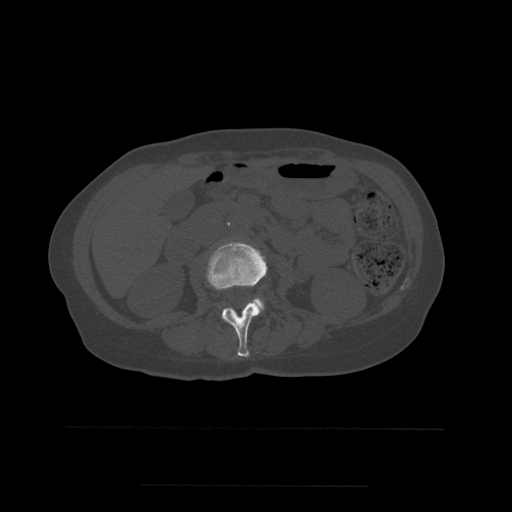
CT including the spine, one axial slice. Slice 204 of 544 in the series (ordered by position). Bone window (W 1800 / L 400 HU). 512 × 512 image matrix, field of view 350 × 350 mm. Patient age 58 years. From the clinical record (not read from this slice): primary cancer: lung.
Outlined on this slice (semi-automatic segmentation, software-assisted and operator-edited):
- L2 vertebra: box from (x=206, y=242) to (x=268, y=358) px